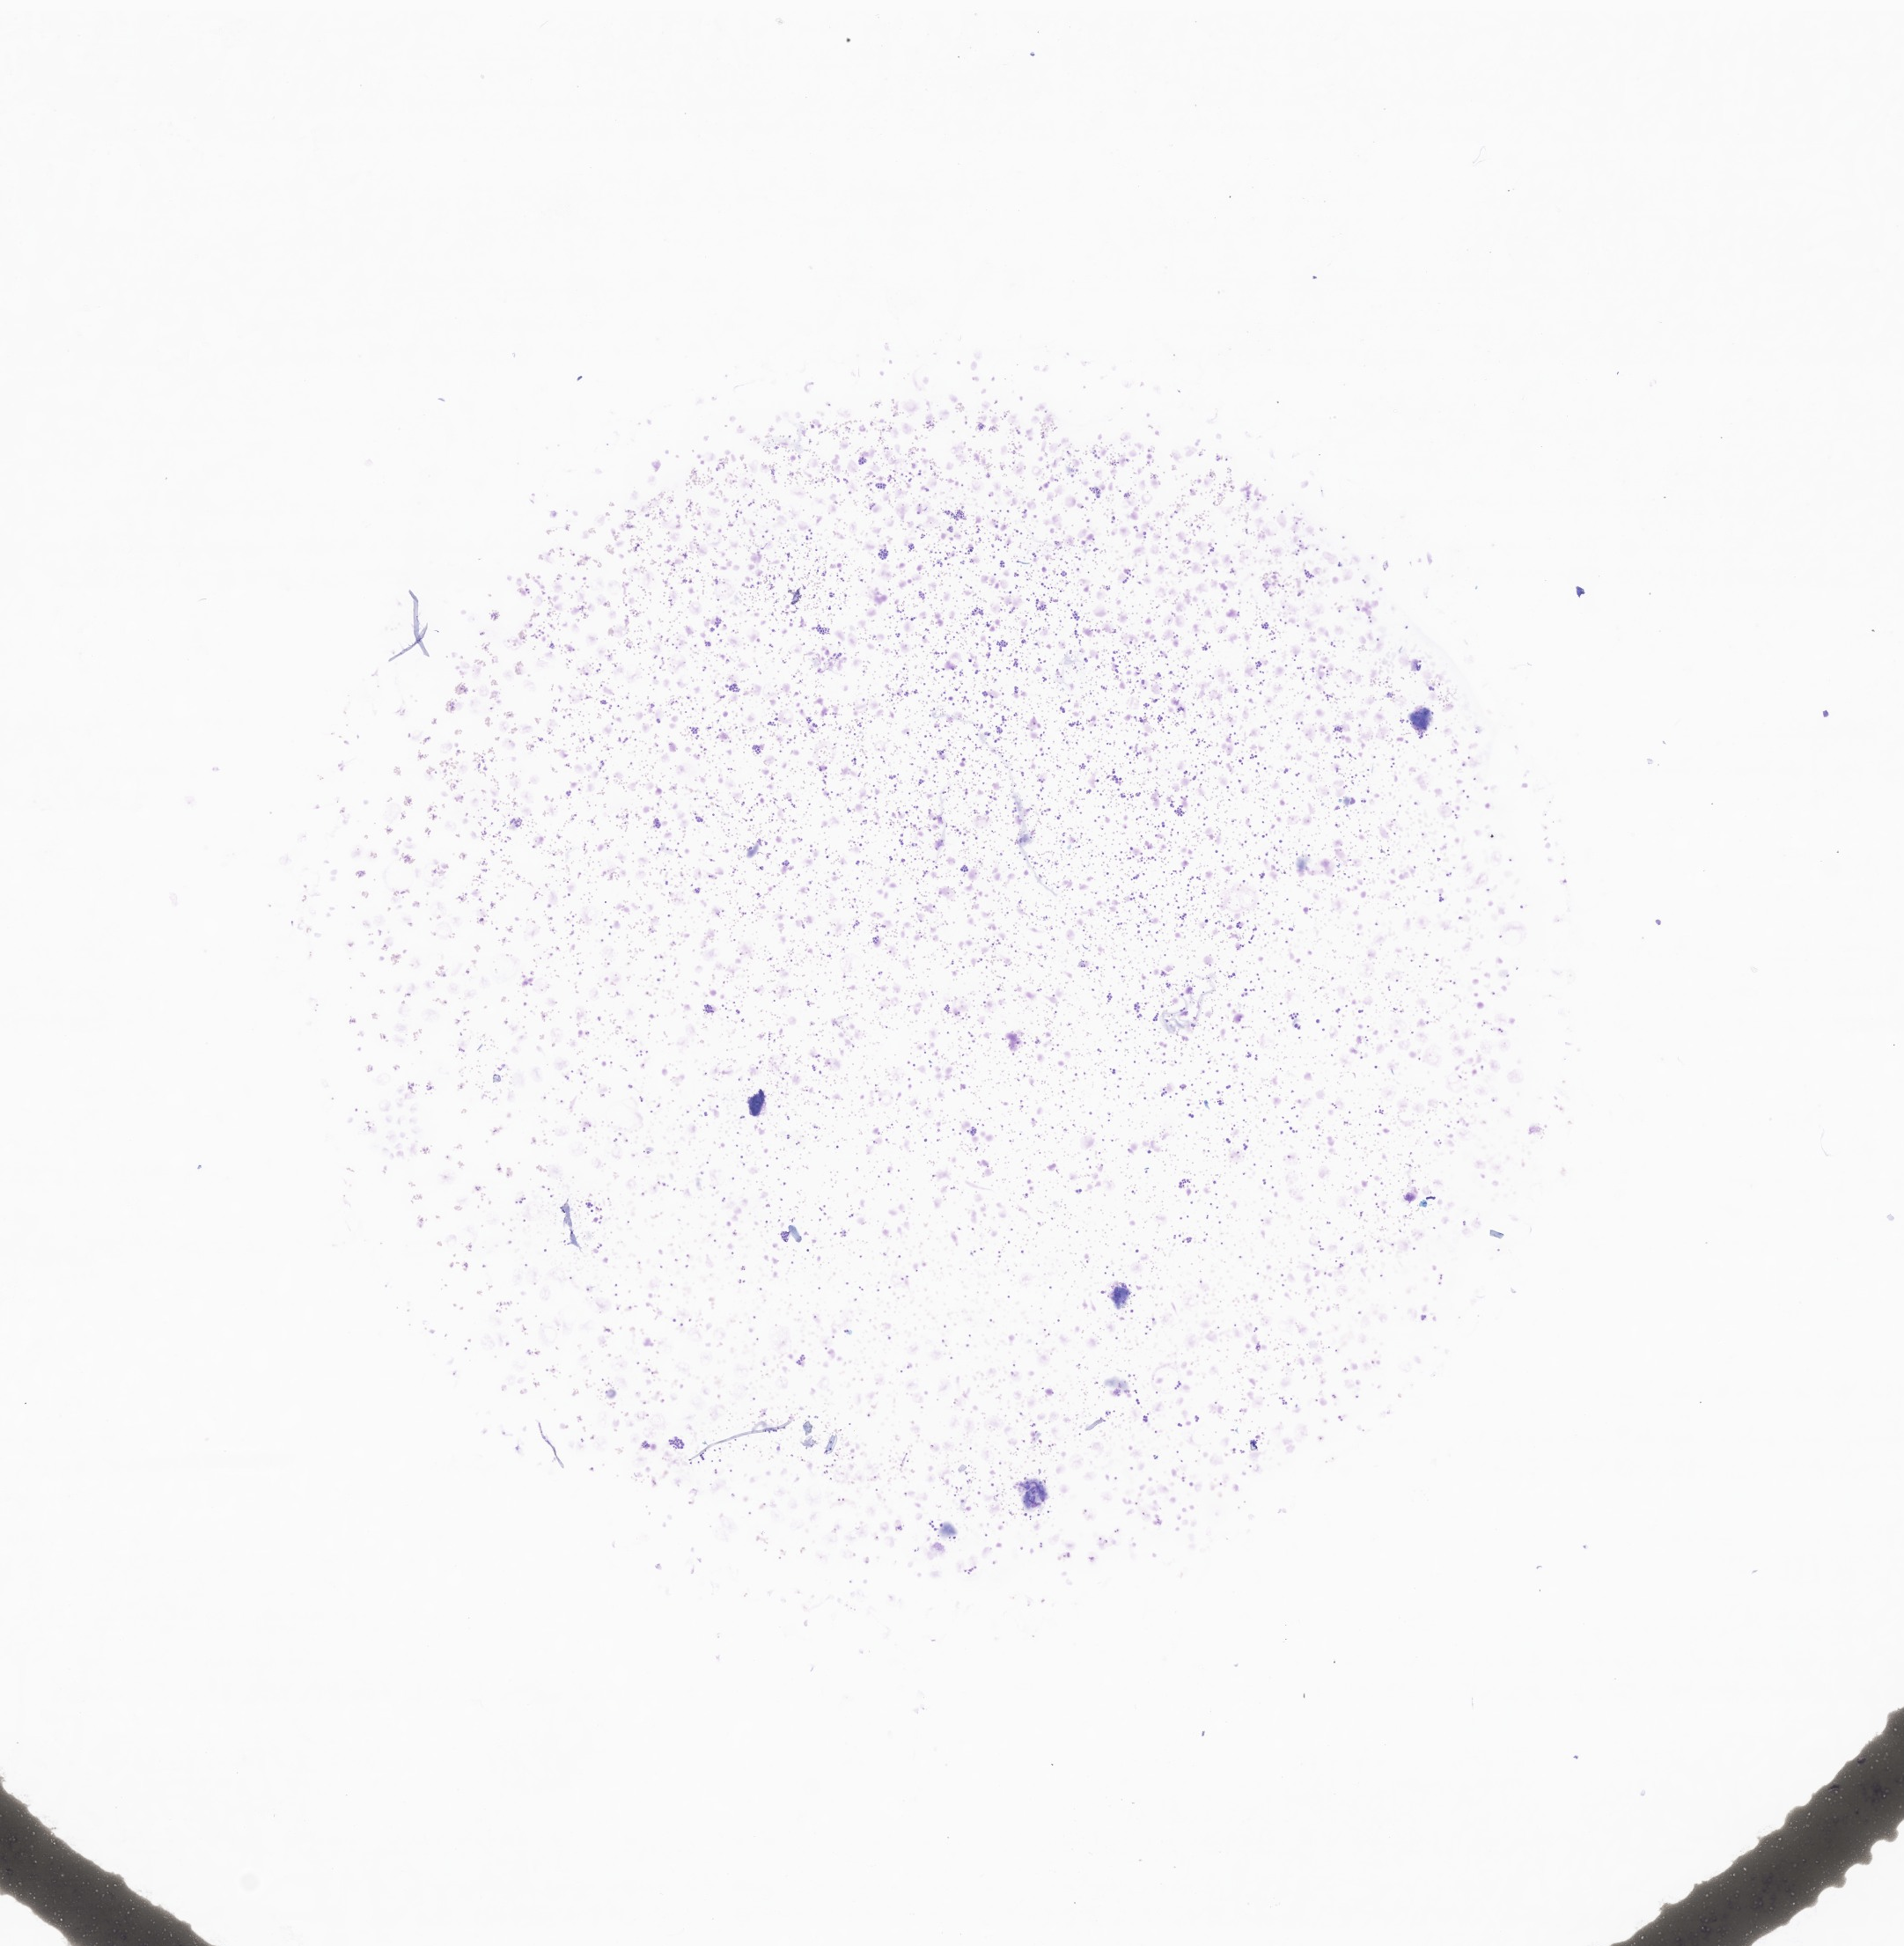
Whole-slide image of tumor tissue from the adrenal gland, a low-resolution overview of the entire scanned area, about 9.1 x 9.3 mm. Patient female; age 609 days (about 1.7 years).
Diagnosis: Neuroblastoma, NOS.